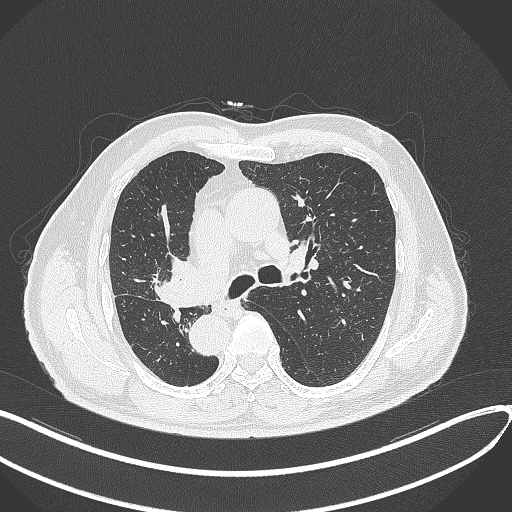
Chest CT, one axial slice. Position 185 of 300 along the scan axis. Reconstruction kernel B70f. 120 kVp. Lung window (W 1500 / L -600 HU). 1 mm slice thickness. 512 × 512 image matrix. Male patient, age 67 years. From the clinical record (not read from this slice): clinical TNM (as recorded): T2a N0 M0.
Annotated regions visible in this slice (rectangle marked by the reading radiologist):
- lung tumour (recorded histology: squamous cell carcinoma): bounding box [x1, y1, x2, y2] px = [152, 248, 201, 309]